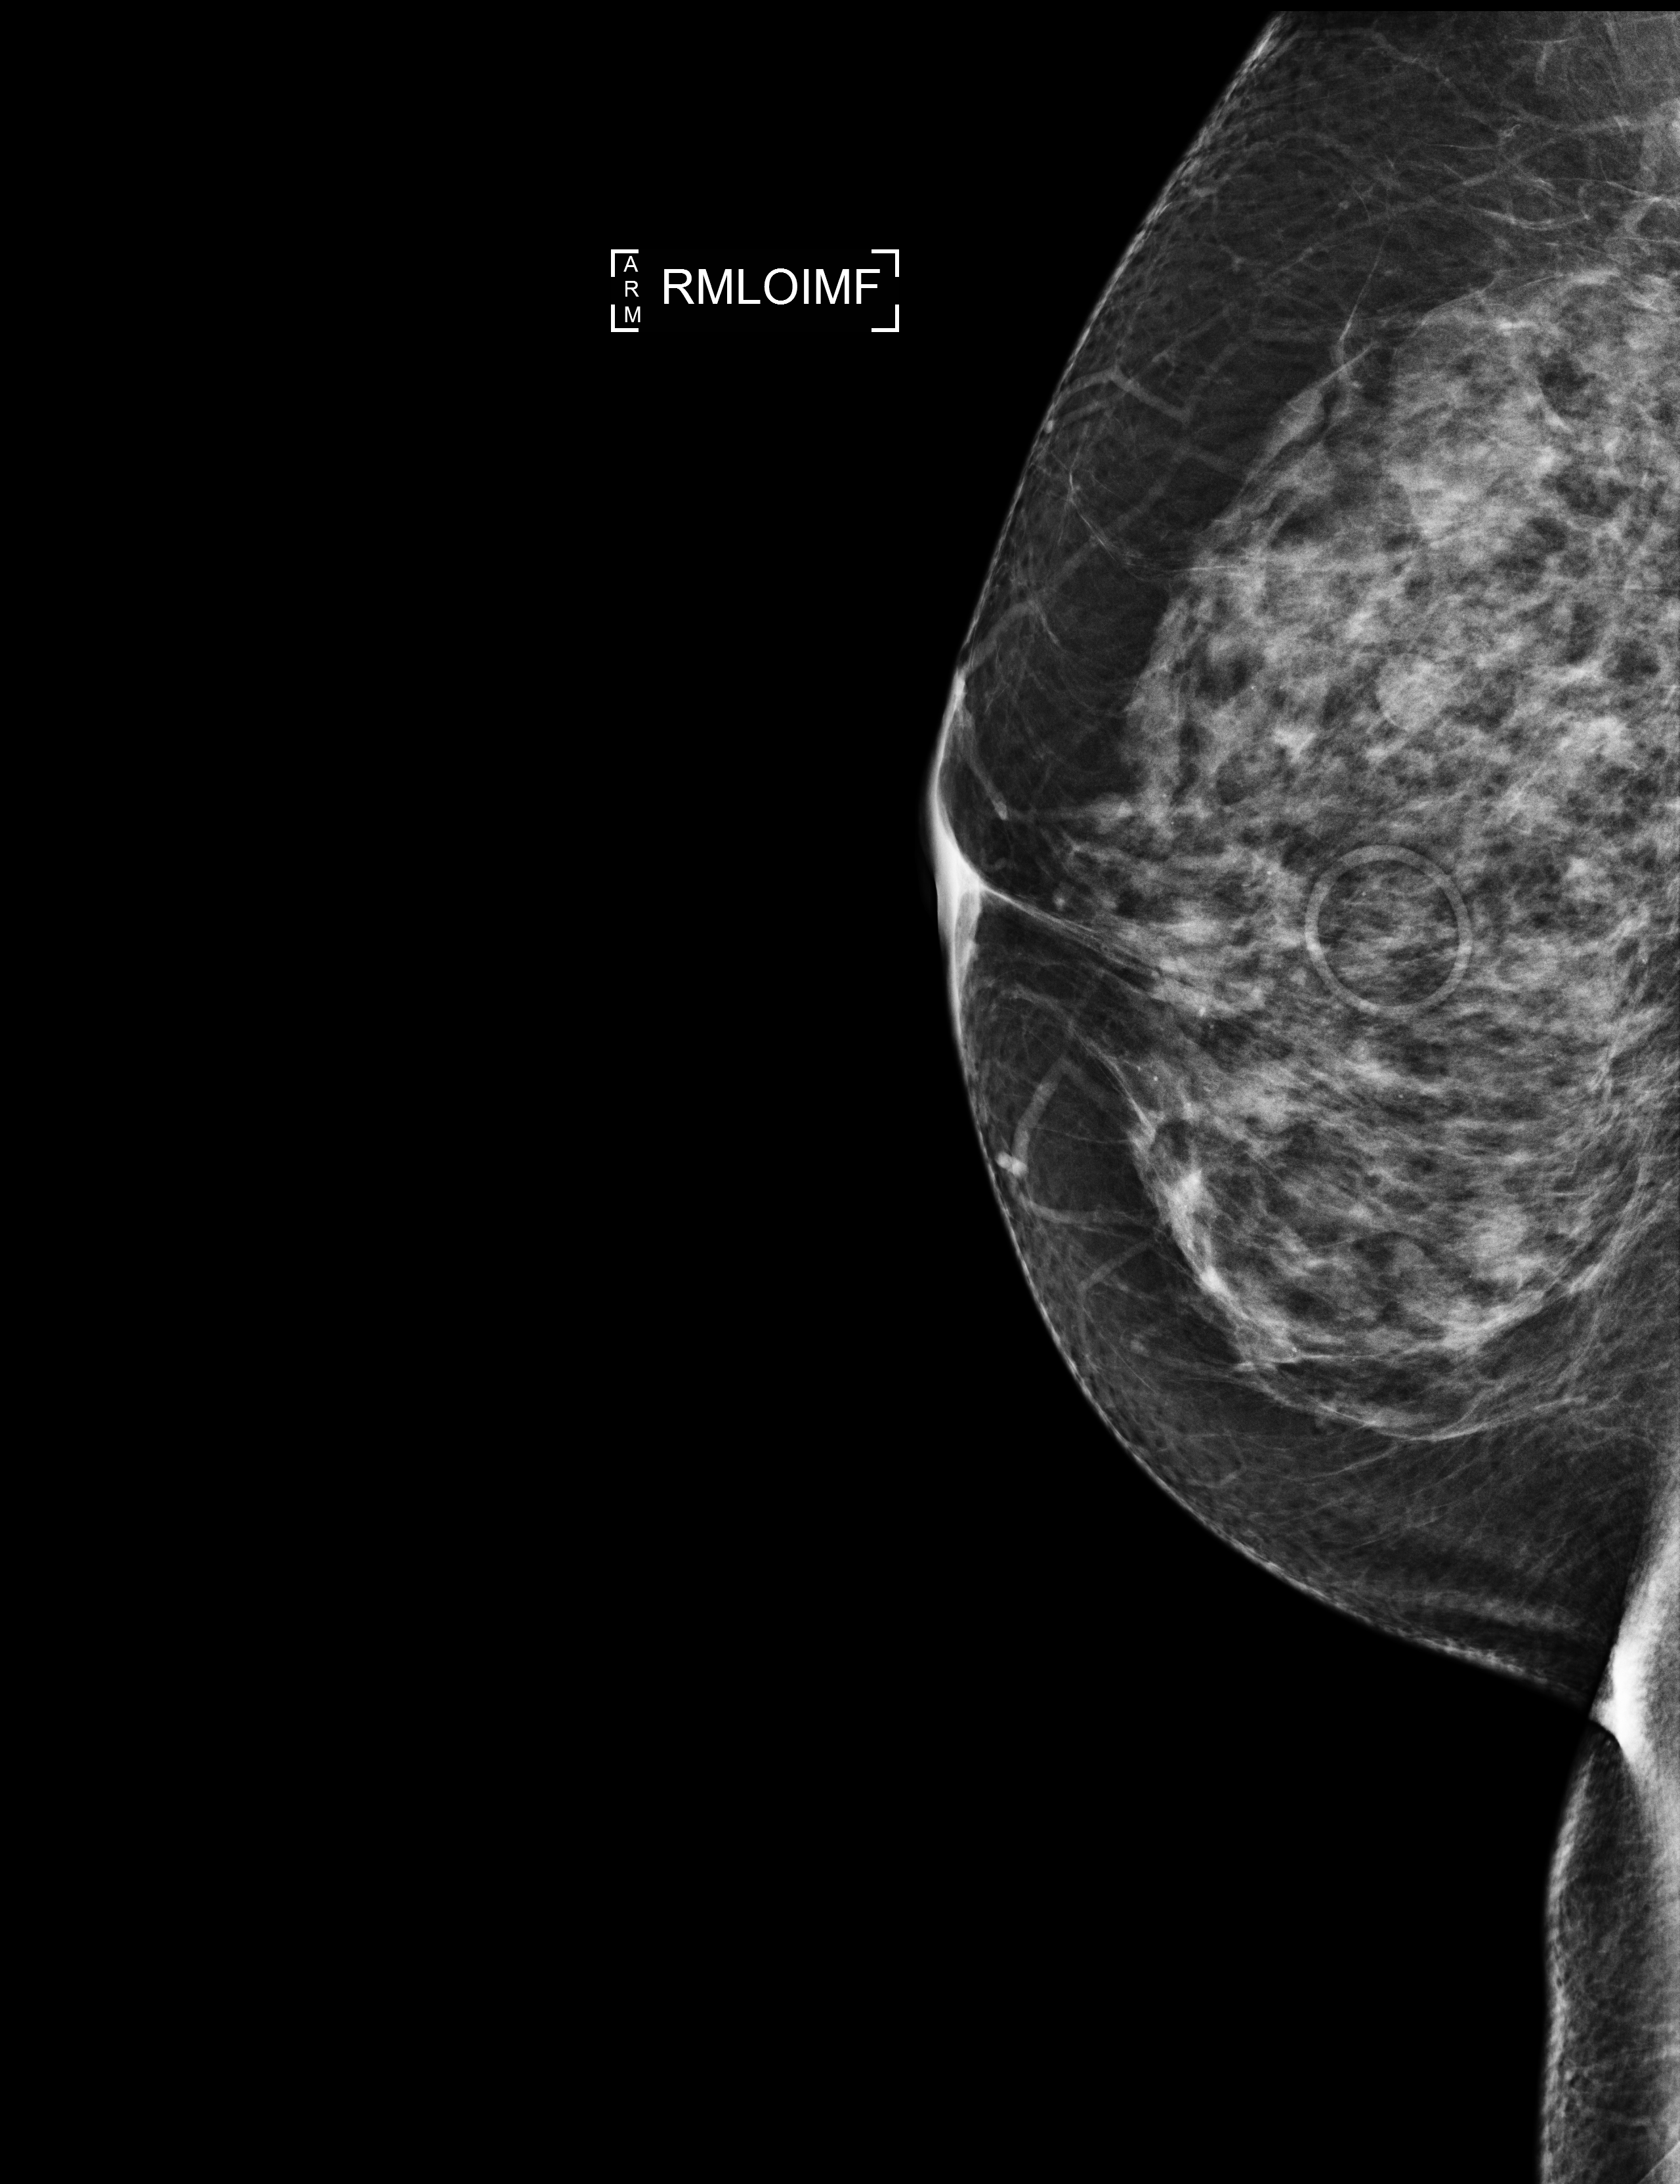
Annual screening mammography examination; compressed breast thickness 65 mm; system: Selenia Dimensions.
Image type: full-field digital mammogram. Breast: right. Projection: mediolateral oblique (MLO) view, infra-mammary fold.